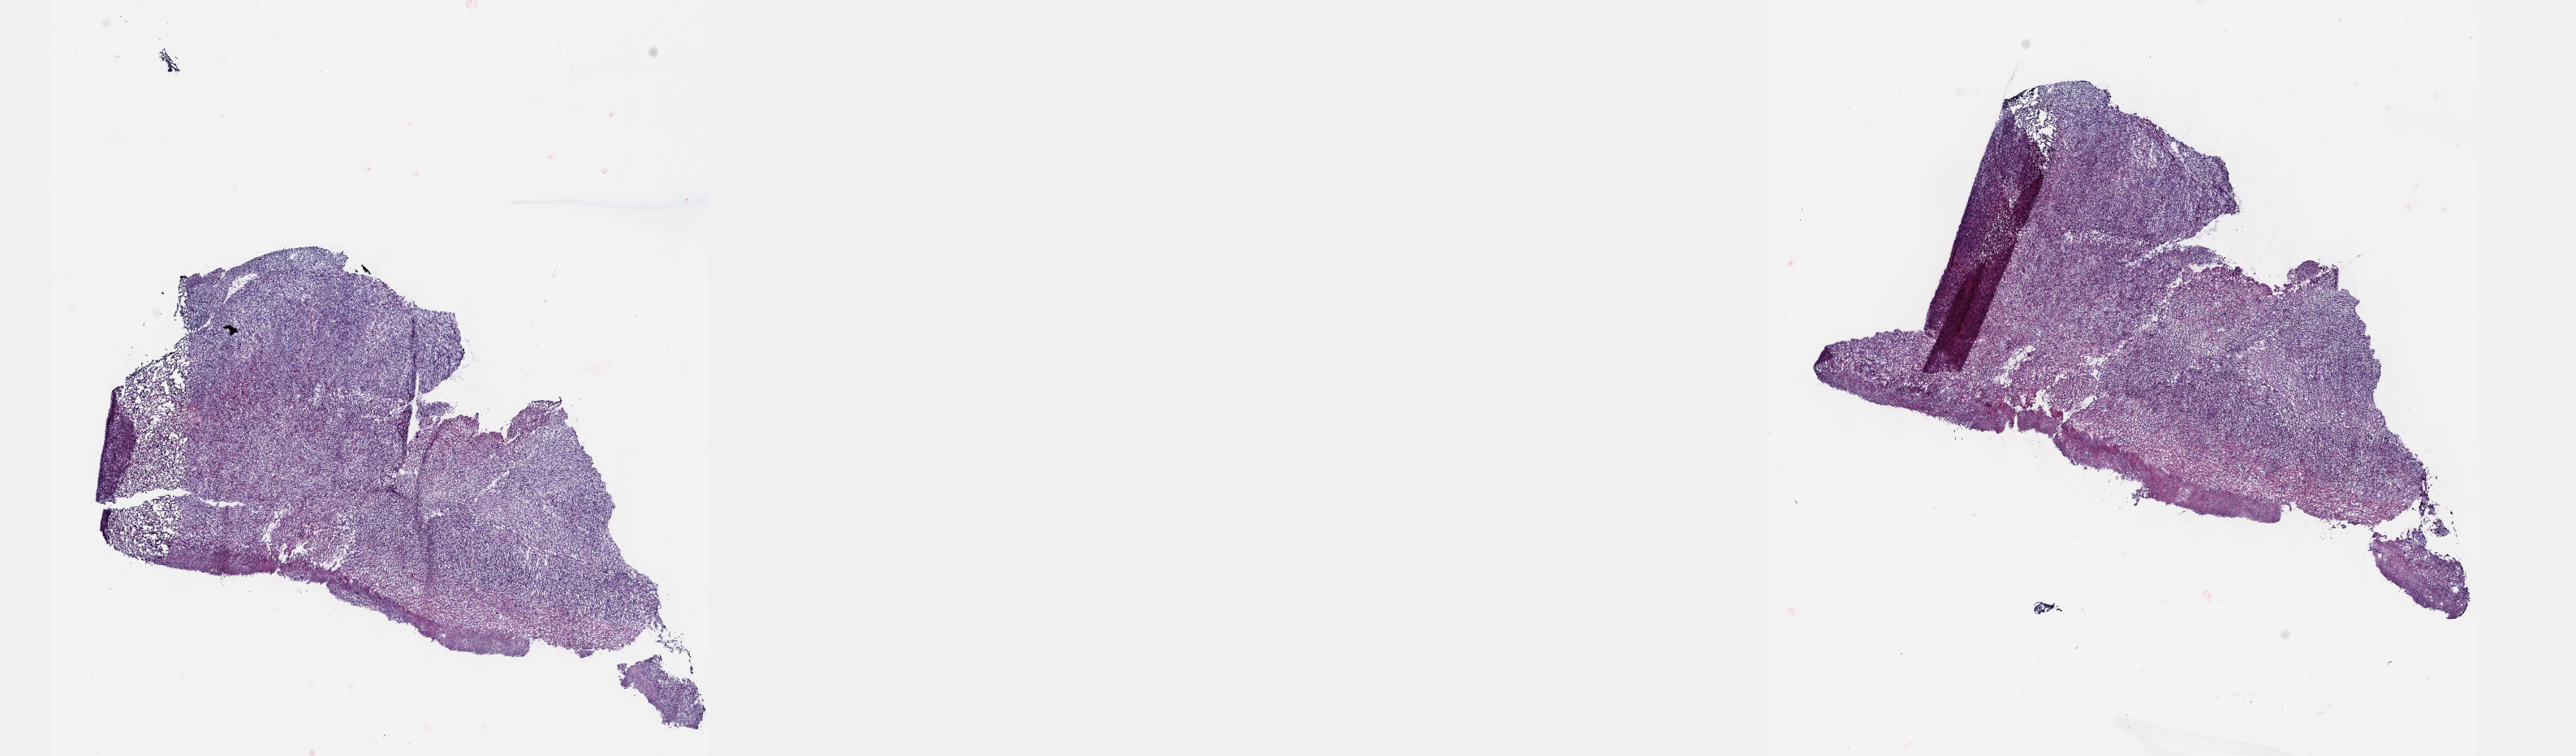
Digitized H&E-stained tissue section (whole slide), low-resolution overview of the scanned area, about 25.7 x 7.5 mm. Frozen section. Sample: primary tumour, lymphoid tissue. Female patient; age at initial diagnosis 63 years. Slide review estimates, as recorded: tumour cells 60%, tumour nuclei 80%, normal cells 0%, stromal cells 30%, necrosis 10%. Inflammatory infiltration, as recorded: lymphocyte infiltration 80%, monocyte infiltration 5%, neutrophil infiltration 5%.
* histologic diagnosis: Primary diffuse large B-cell lymphoma of the CNS (cerebellum, NOS)